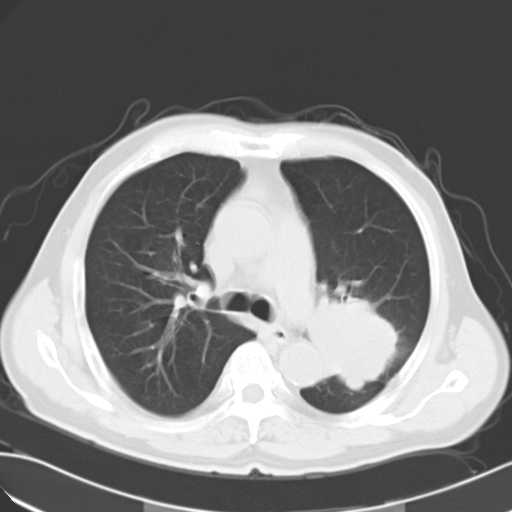
Chest CT, one axial slice; slice 18 of 28 in the series (ordered by position); reconstruction kernel B40f; 120 kVp; lung window (W 1500 / L -600 HU); 10 mm slice thickness; 512 × 512 image matrix, field of view 353 × 353 mm. Patient: male, 63 years. Case-level facts recorded for this patient, not image findings: clinical TNM (as recorded): T3 N3 M1a; histopathological grade: G3.
Structures marked on this image (bounding box drawn by a radiologist):
- lung tumour (recorded histology: large cell carcinoma): bounding box <304,292,407,409> (left, top, right, bottom; pixels)